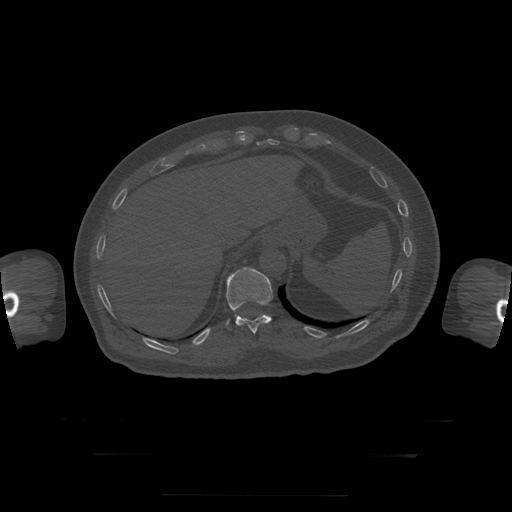
CT including the spine, one axial slice; reconstruction kernel STANDARD; 120 kVp; bone window (W 1800 / L 400 HU); 1.25 mm slice thickness; 512 × 512 image matrix, field of view 510 × 510 mm. Patient age 73 years. From the clinical record (not read from this slice): primary cancer: prostate.
Structures marked on this image (semi-automatic segmentation, software-assisted and operator-edited):
- T11 vertebra: bounding box (x1, y1, x2, y2) in pixels: (226, 267, 273, 334)
- T12 vertebra: (265, 315, 270, 317)